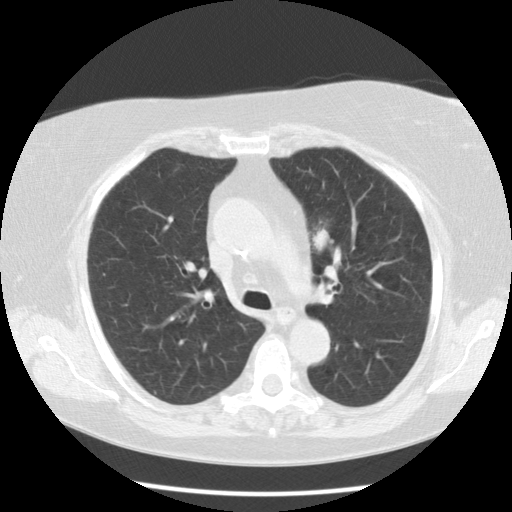
Low-dose screening chest CT, one axial slice; position 78 of 109 along the scan axis; reconstruction kernel STANDARD; 120 kVp; lung window (W 1500 / L -600 HU); 2.5 mm slice thickness; 512 × 512 image matrix.
Annotated regions visible in this slice (expert manual segmentation):
- lesion 1 (tumor, upper lobe of left lung): bounding box (x1, y1, x2, y2) in pixels: (312, 228, 333, 251)